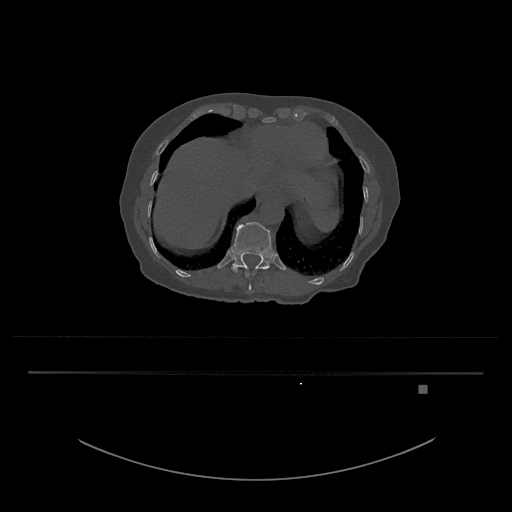
CT including the spine, one axial slice. Position 630 of 797 along the scan axis. Reconstruction kernel Br40s/3. 120 kVp. Bone window (W 1800 / L 400 HU). 0.5 mm slice thickness. 512 × 512 image matrix, field of view 500 × 500 mm. Patient: female, 57 years. From the clinical record (not read from this slice): primary cancer: cervical.
Annotated regions visible in this slice (semi-automatically segmented with operator editing):
- T11 vertebra: box from (x=245, y=268) to (x=260, y=291) px
- T12 vertebra: (x=231, y=222)–(x=274, y=273)